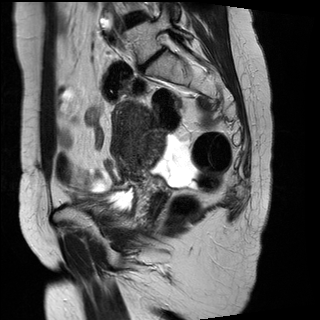
Pelvic MRI for cervical cancer, one sagittal slice; position 19 of 29 along the scan axis; T2-weighted; 1.5 T; TE 89 ms, TR 2930 ms; 4 mm slice thickness; 320 × 320 image matrix, field of view 260 × 260 mm. Female patient, age 45 years.
Outlined on this slice (expert manual segmentation):
- uterus and cervix: bounding box (x1, y1, x2, y2) in pixels: (110, 99, 167, 180)